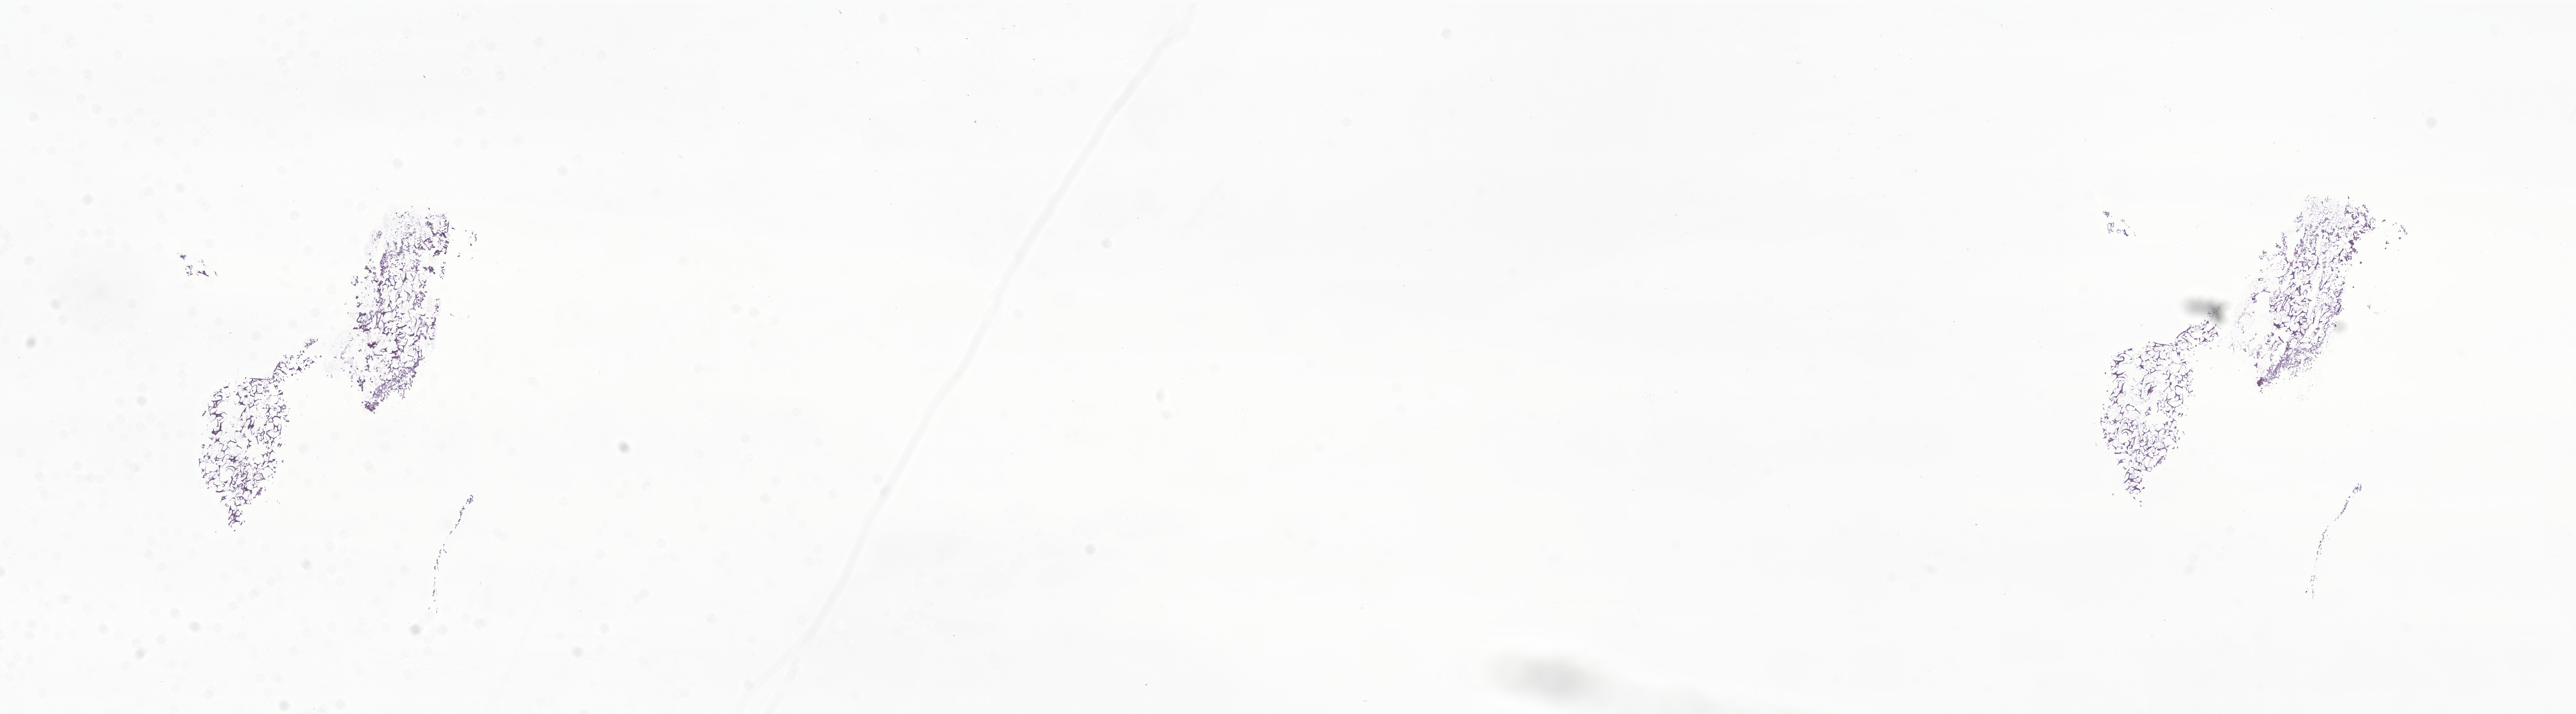
Digitized hematoxylin and eosin (H&E)-stained section of tumor tissue from the cerebellum, a low-resolution overview of the entire scanned area, about 24.2 x 6.7 mm. Frozen section (OCT-embedded). Patient male; age 87 months (7 years 3 months).
Recorded diagnosis: Medulloblastoma, NOS.